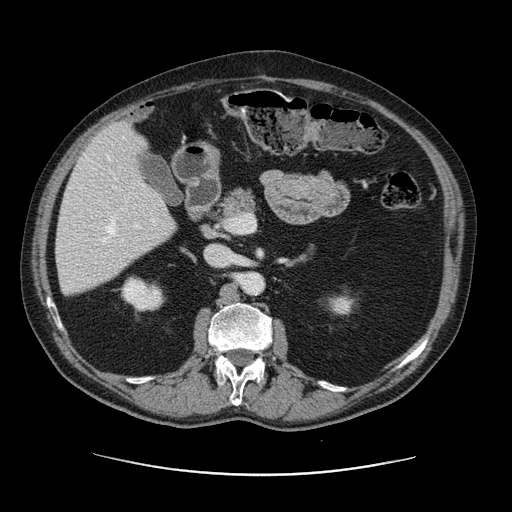
Contrast-enhanced abdominal CT, one axial slice; position 62 of 141 along the scan axis; 120 kVp; soft-tissue window (W 400 / L 40 HU); 2.5 mm slice thickness; 512 × 512 image matrix. Male patient, age 72 years. Case-level facts recorded for this patient, not image findings: diagnosis: colorectal cancer liver metastases, imaged before liver resection; multiple liver metastases: yes; largest metastasis: 5.4 cm; chemotherapy before resection: yes.
Outlined on this slice (outlined manually by an expert reader):
- hepatic veins: bounding box [x1, y1, x2, y2] px = [101, 136, 125, 242]
- liver: [57, 123, 175, 295]
- planned liver remnant (the part of the liver to remain after resection): [57, 185, 176, 295]
- portal vein (with intrahepatic branches): [109, 212, 143, 239]